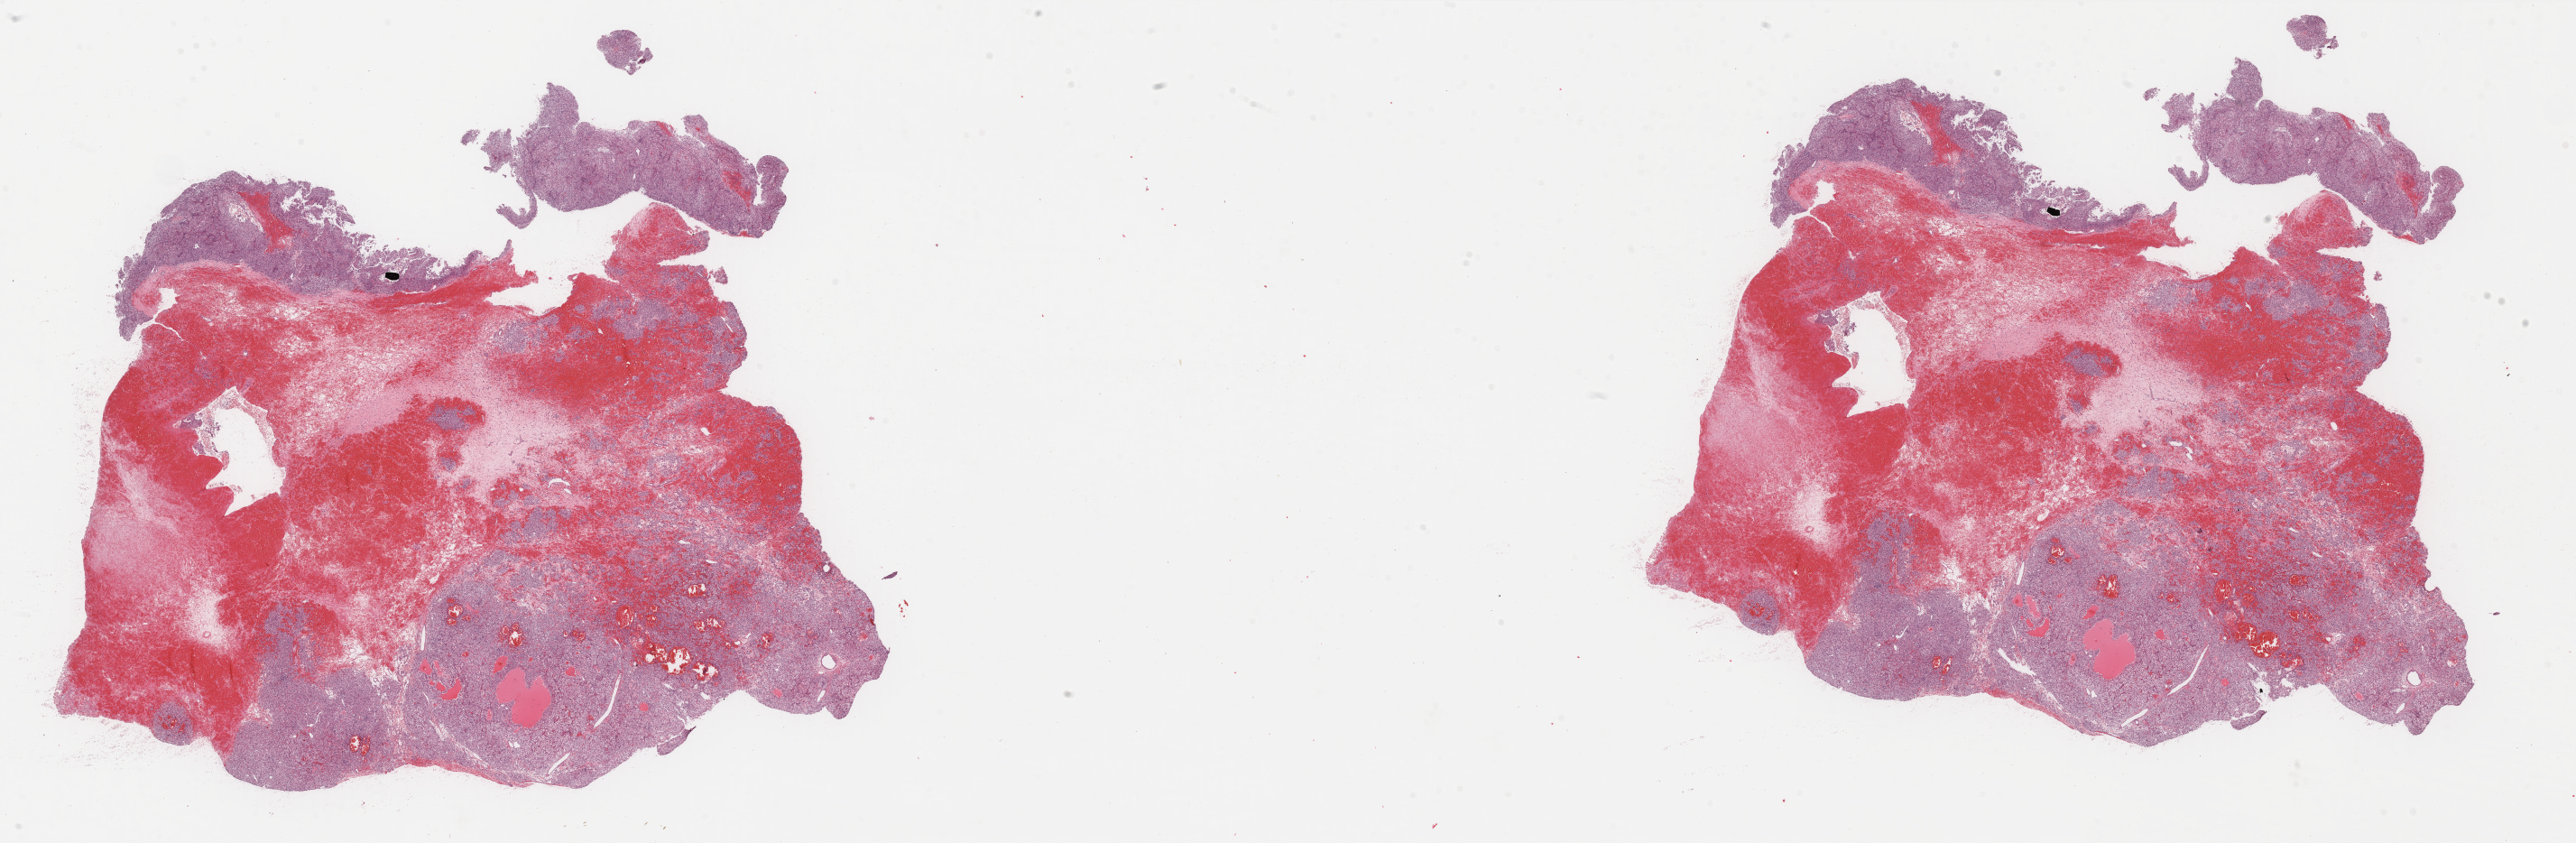
Hematoxylin and eosin (H&E) stained whole-slide image — shown as a low-resolution overview of the whole scanned area (about 45.2 x 14.8 mm), FFPE section, primary tumour sample from the kidney. Male, age 50 years at initial diagnosis. Histologic grade: G3 (poorly differentiated).
• AJCC pathologic stage: I
• TNM: T1a NX MX
• histologic diagnosis: Renal cell carcinoma, NOS